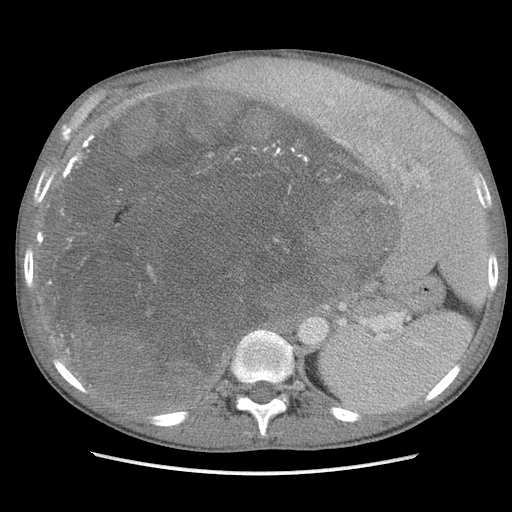
Contrast-enhanced abdominal CT, one axial slice; position 74 of 115 along the scan axis; soft-tissue window (W 400 / L 40 HU); 5 mm slice thickness; 512 × 512 image matrix. Male patient. Case-level facts recorded for this patient, not image findings: diagnosis: adrenocortical carcinoma; tumour side: right adrenal; Ki-67 index: 13 %.
Annotated regions visible in this slice (semi-automatically segmented with operator editing):
- mass: box from (x=46, y=93) to (x=386, y=402) px